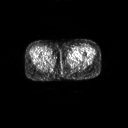
FDG PET of an extremity soft-tissue mass (from a PET/CT study), one axial slice. Position 5 of 267 along the scan axis. 3.27 mm slice thickness. 128 × 128 image matrix, field of view 700 × 700 mm. Patient: female, 47 years. From the clinical record (not read from this slice): histological type: myxofibrosarcoma; grade: intermediate; site of the primary tumour: left thigh.
Annotated regions visible in this slice (expert contour drawn on MRI and transferred to this co-registered scan by the dataset authors):
- gross tumour volume including surrounding oedema: bounding box <69,54,81,60> (left, top, right, bottom; pixels)